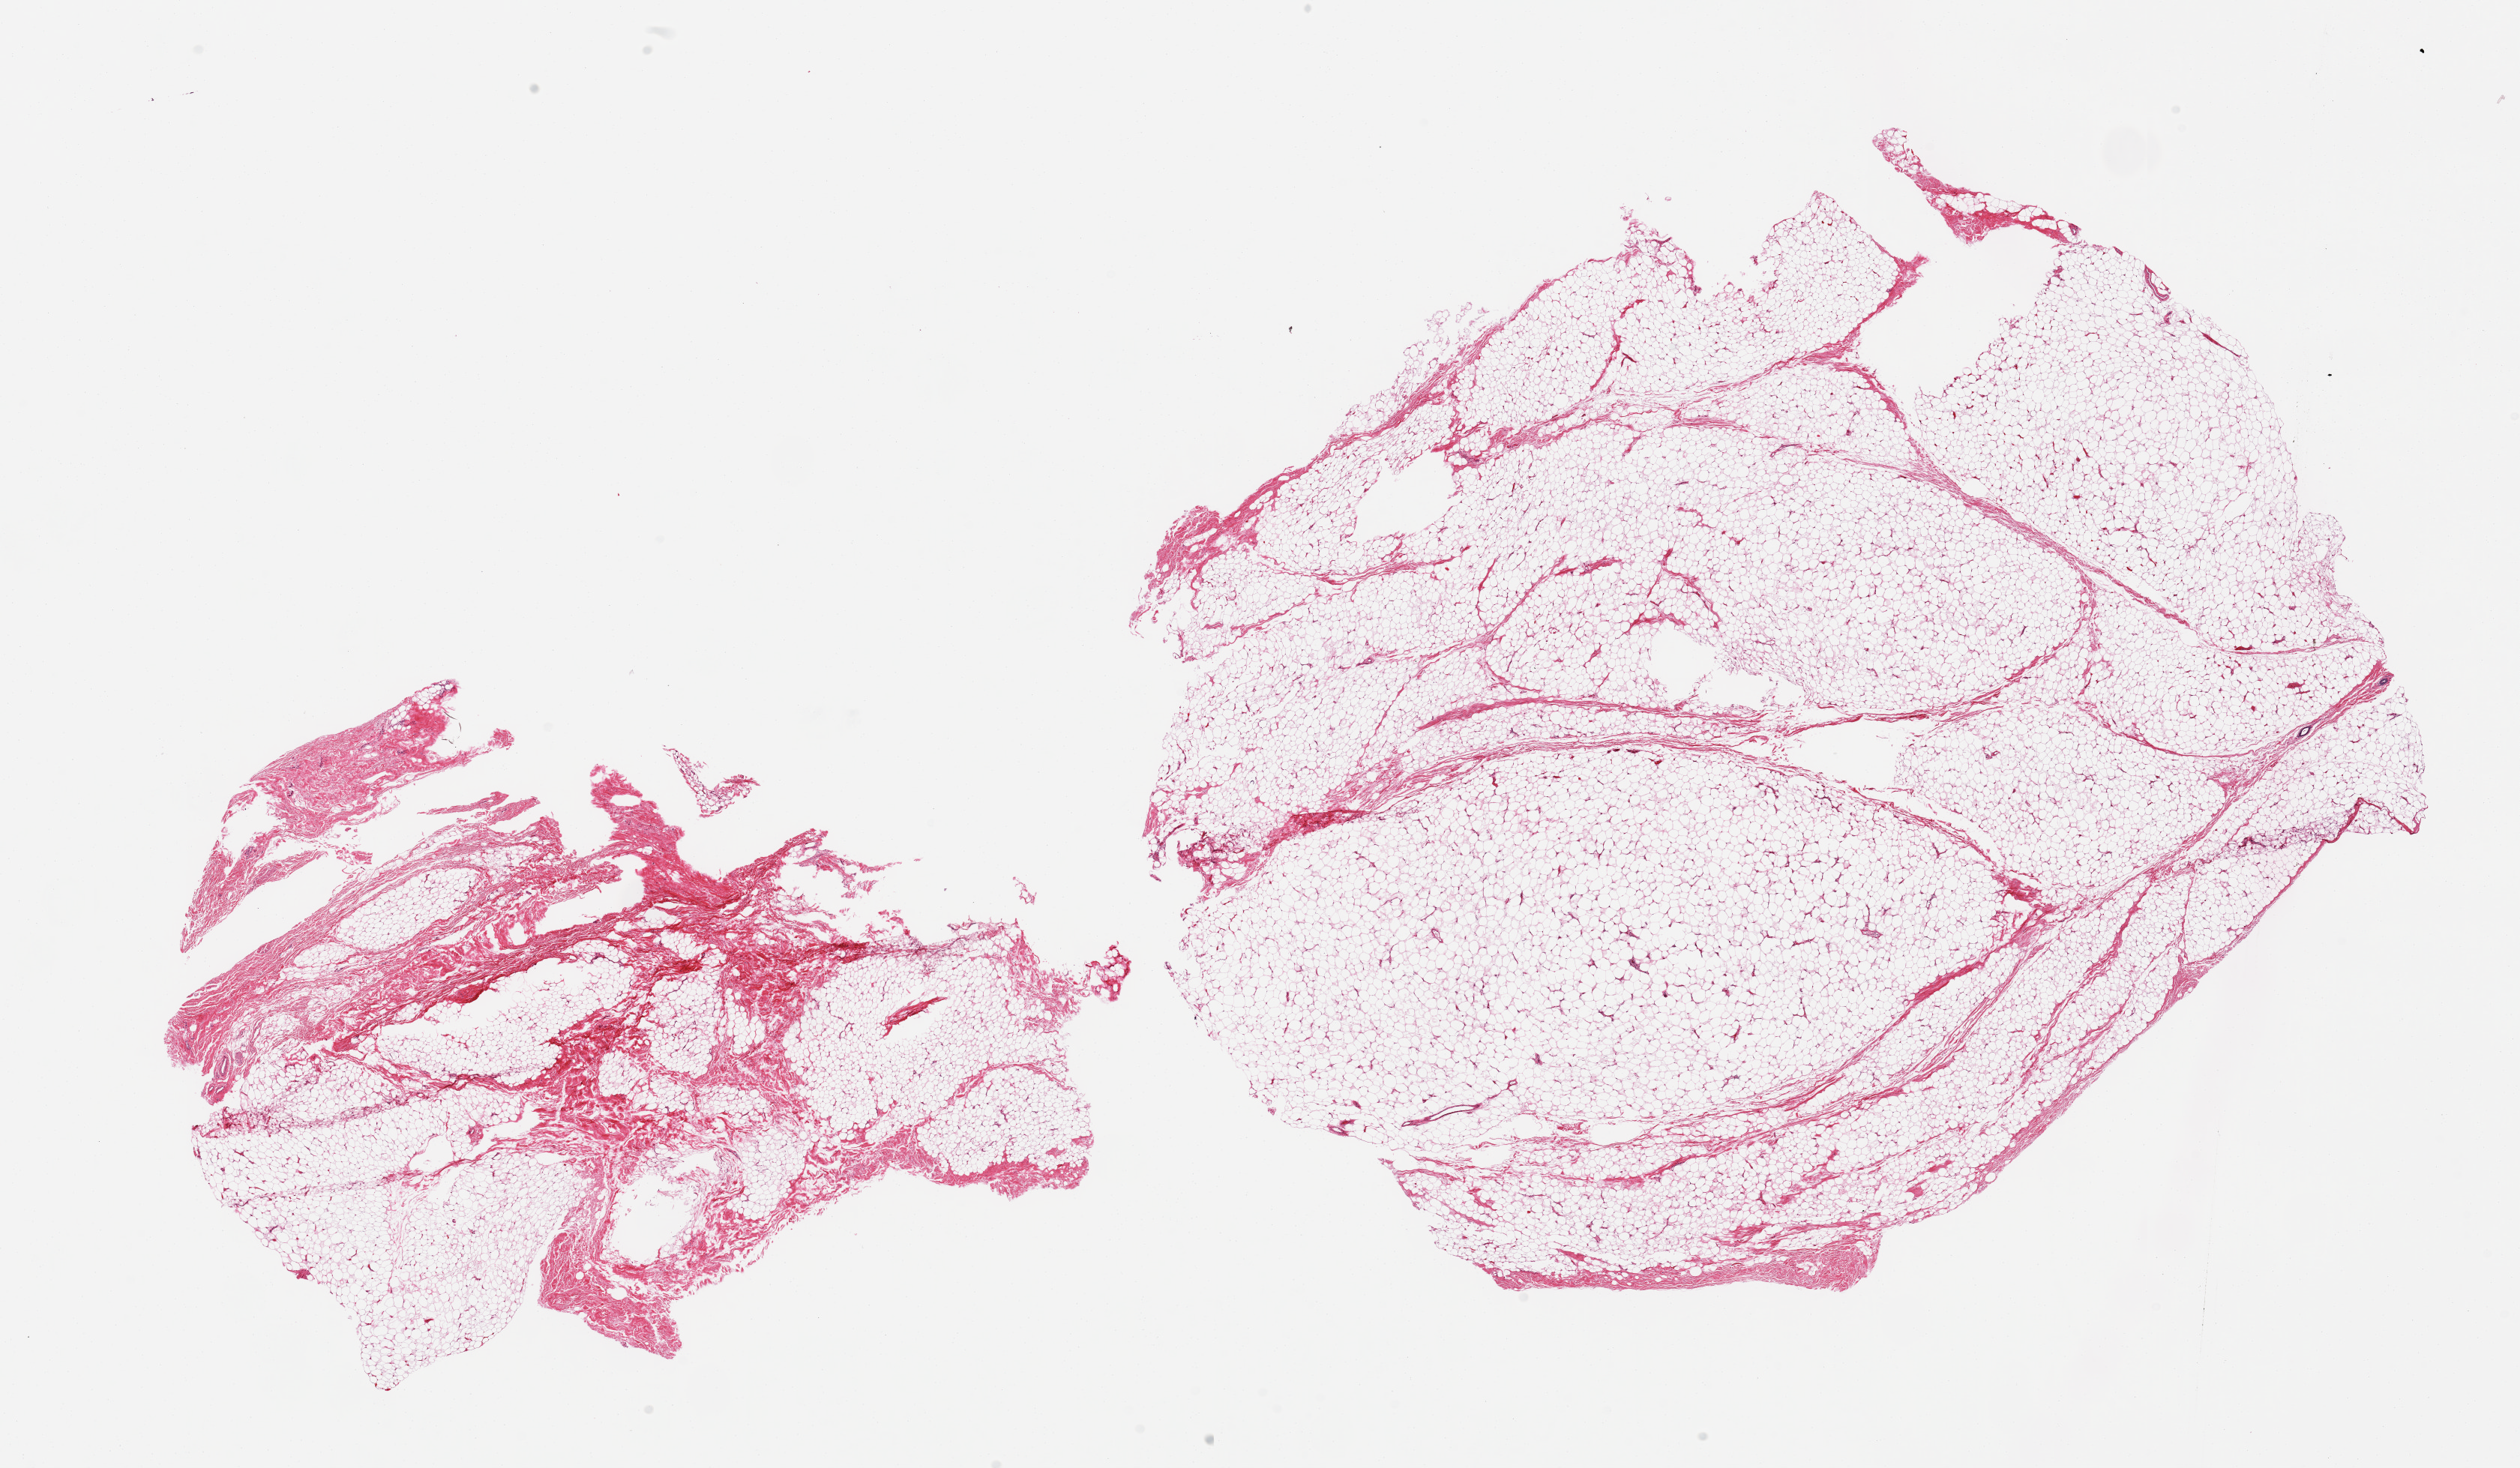
Hematoxylin and eosin (H&E) whole-slide image — whole scanned area (about 26.6 x 15.5 mm, slide scanned at 20x) shown as a low-resolution overview. PAXgene-fixed, paraffin-embedded tissue. Sampled site (target tissue): breast. Tissue donor sample. Male donor.
Reviewer comment on this tissue sample: 2 pieces of fibrofatty tissue without mammary ducts.